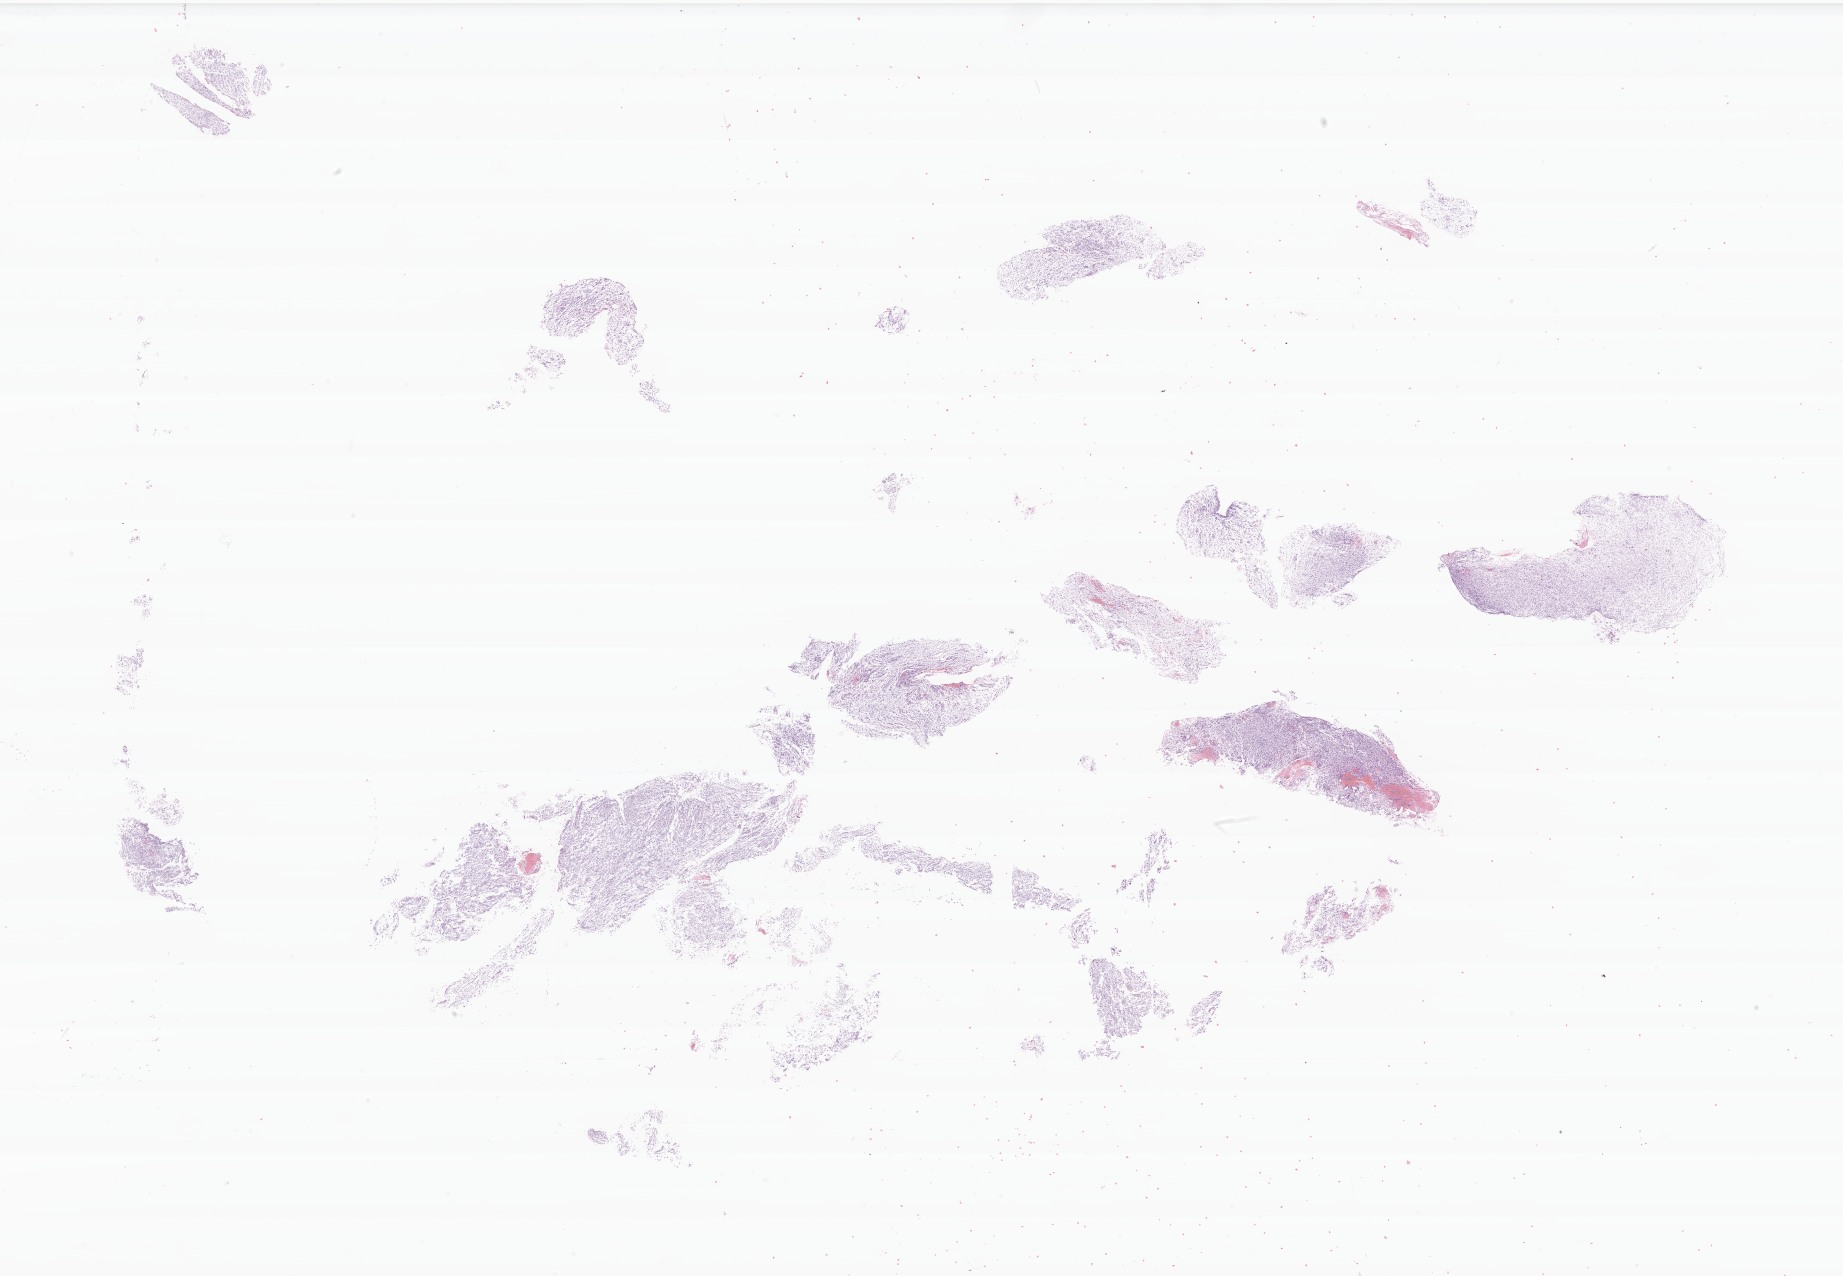
Whole-slide image, haematoxylin and eosin stain of tumor tissue from the brain, whole scanned area (about 31.0 x 21.5 mm) shown as a low-resolution overview. Formalin-fixed, paraffin-embedded (FFPE) tissue. Patient: male, age 204 months (17 years).
Diagnosis (ICD-O-3 morphology term): Neoplasm, malignant.